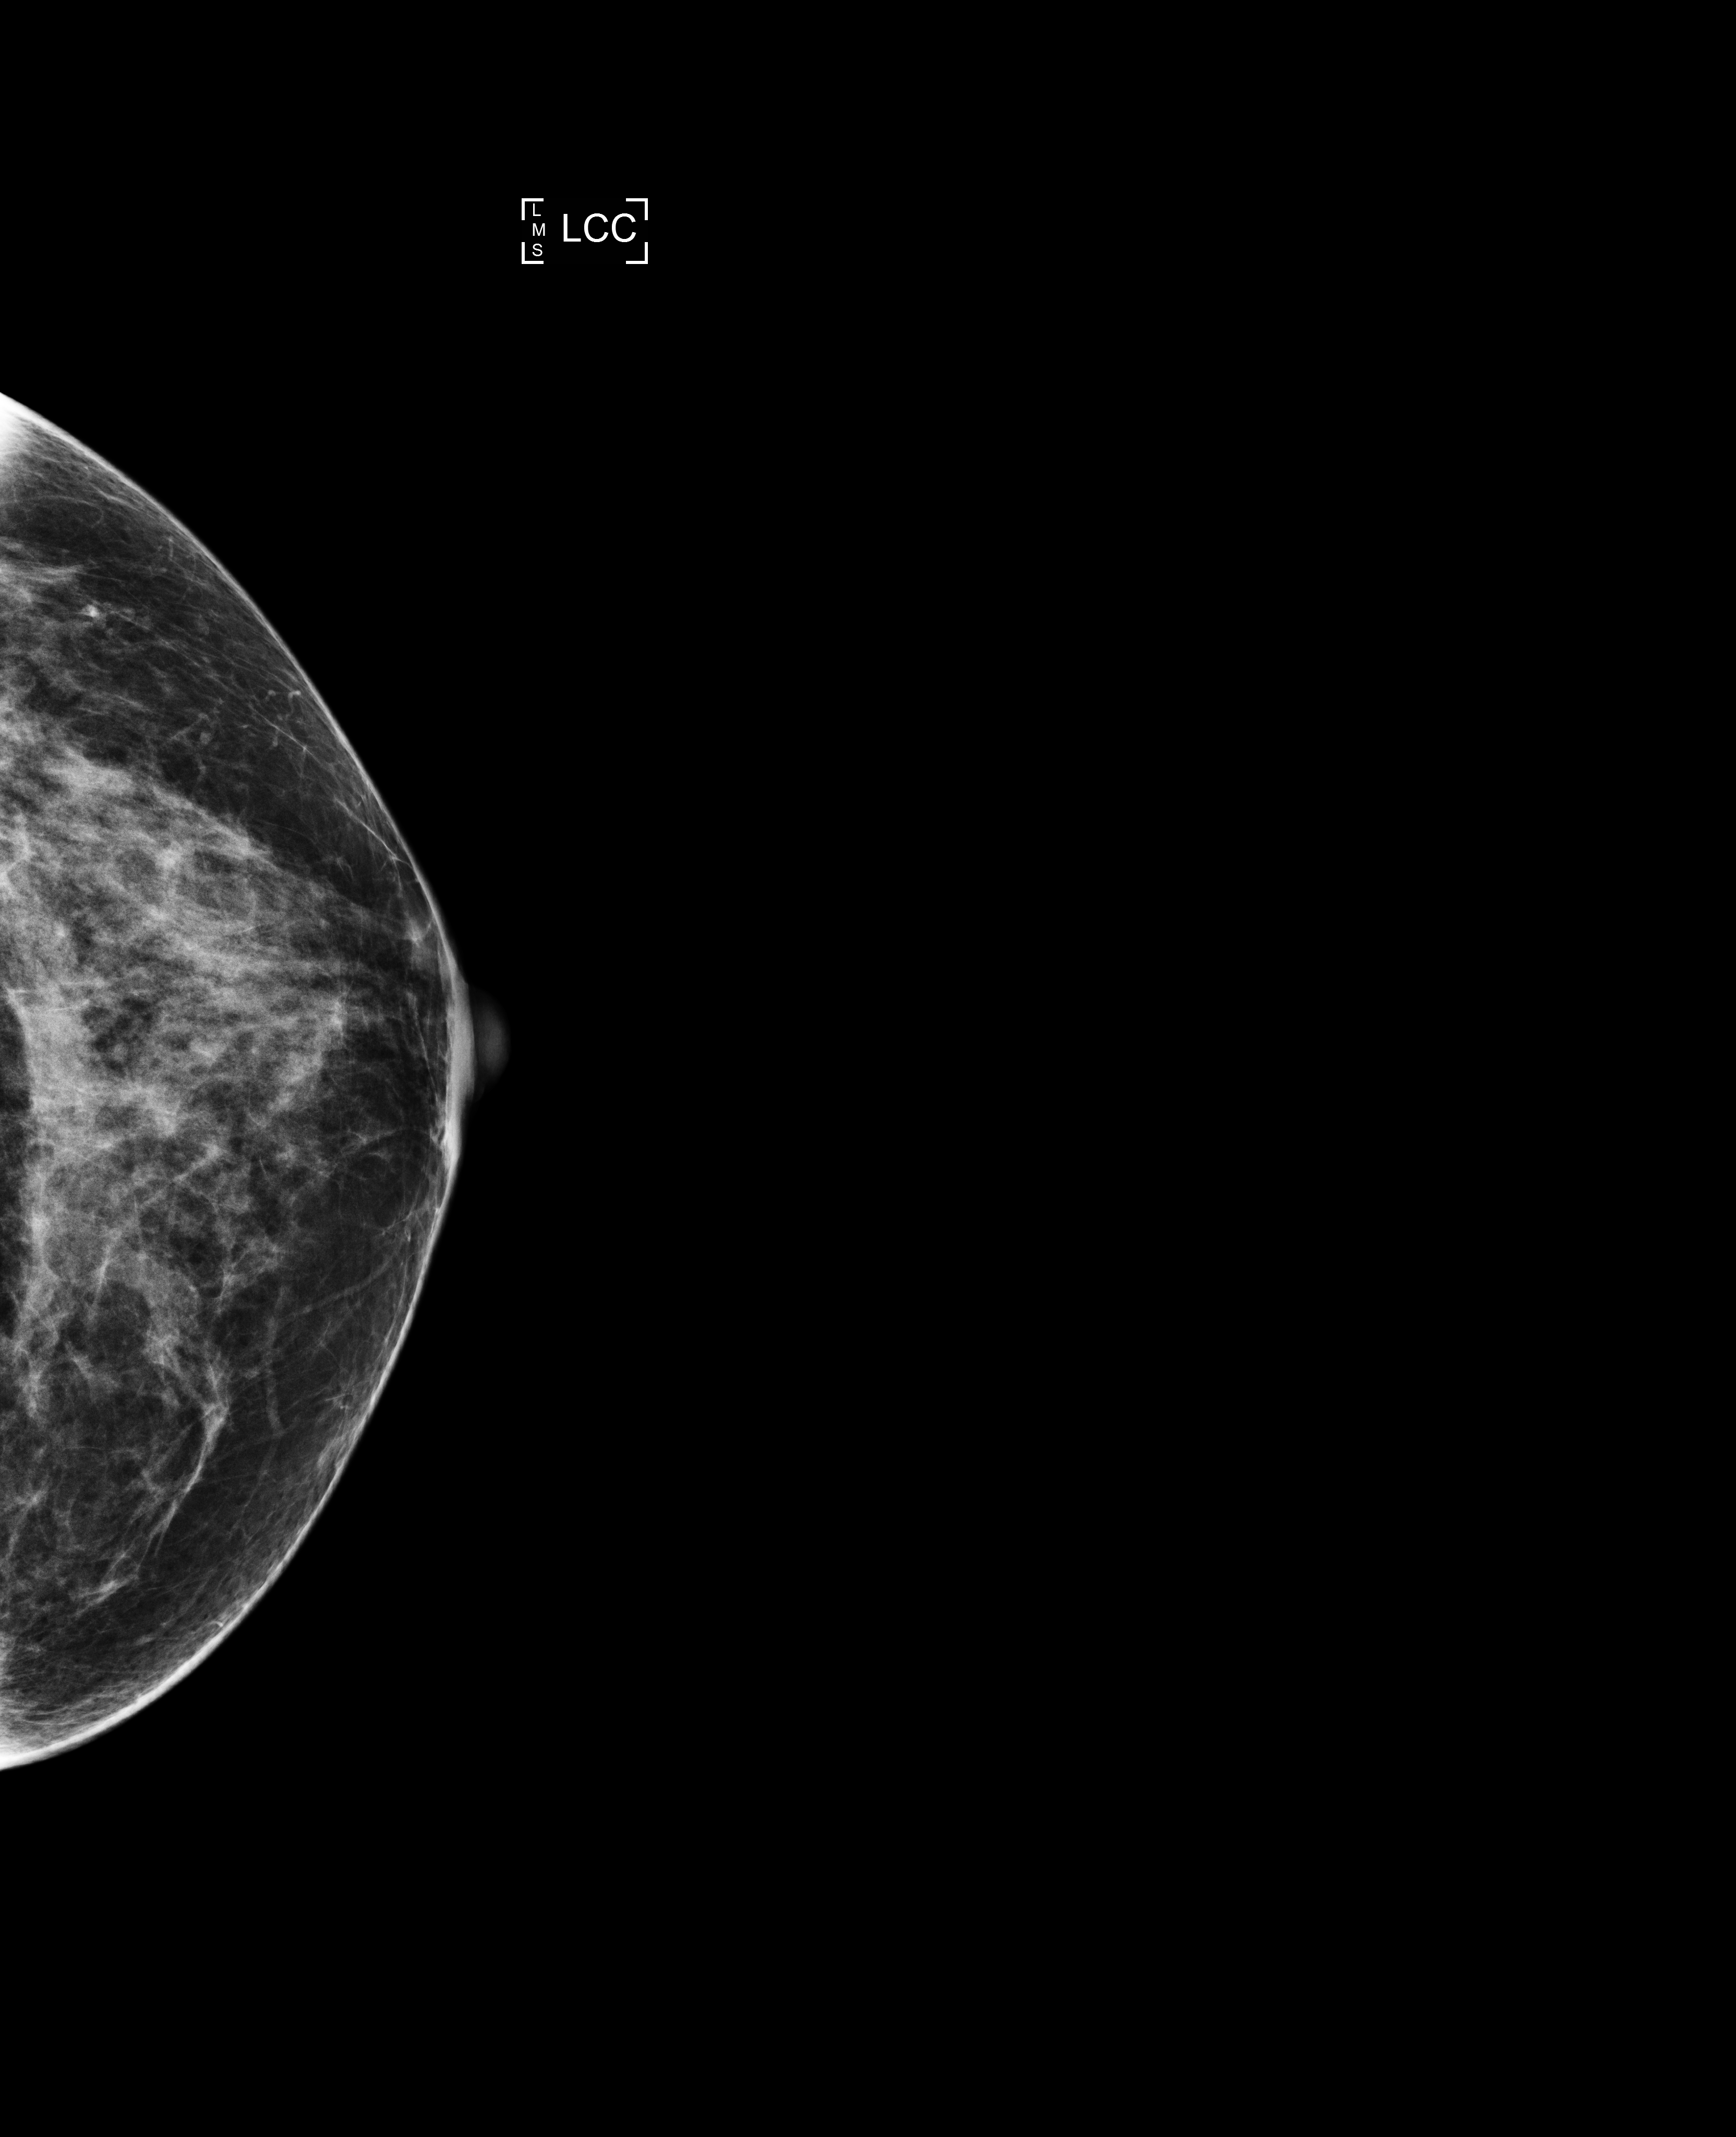
Full-field digital mammogram (FFDM); left breast; craniocaudal (CC) view; annual screening mammography examination; system: Selenia Dimensions. Patient aged 59 years (female).
Final BI-RADS category for the screening round (tomosynthesis exam, both breasts): category 1.